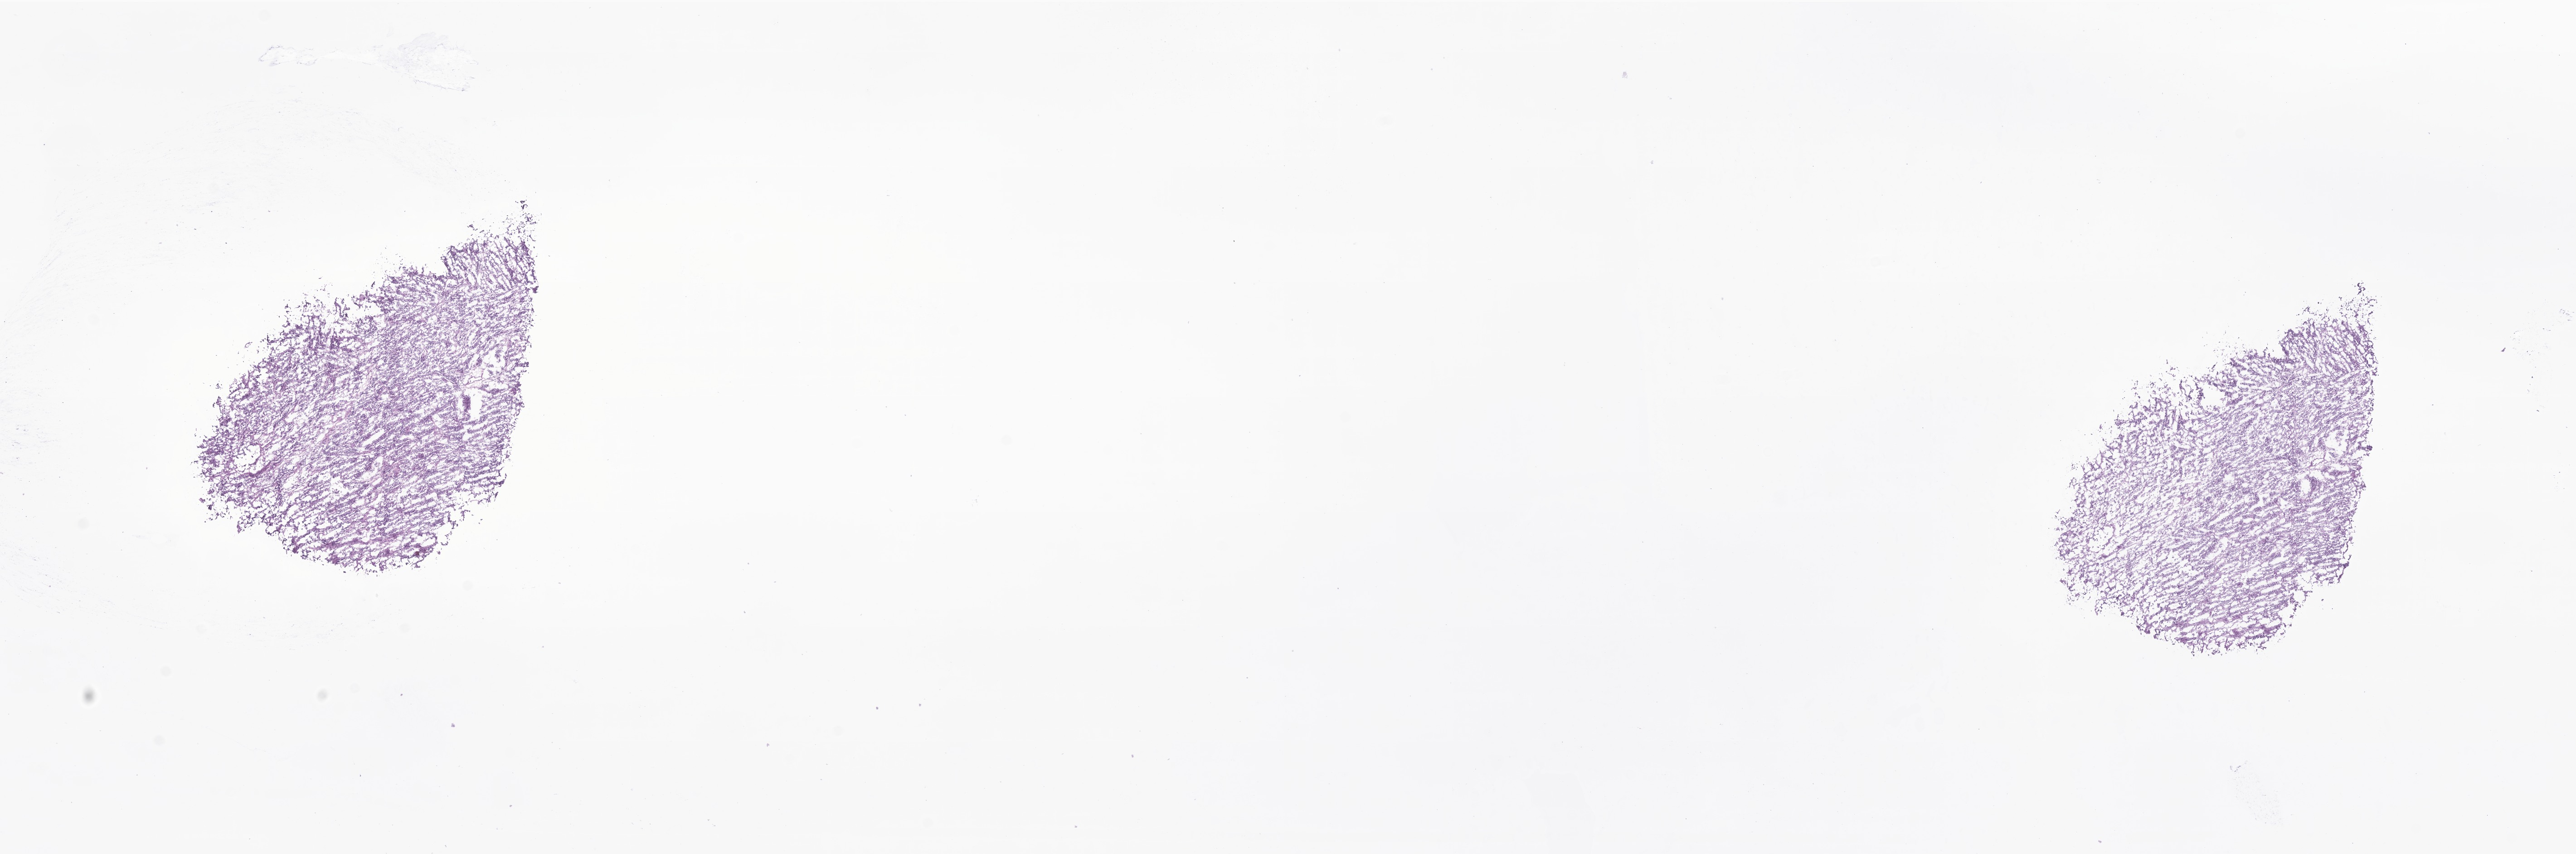
Whole-slide image, hematoxylin and eosin (H&E) stain of tumor tissue from the retroperitoneum, shown as a low-resolution overview of the whole scanned area (about 24.0 x 7.9 mm); frozen section. Female patient, age 20 days.
Recorded diagnosis: Neuroblastoma, NOS.